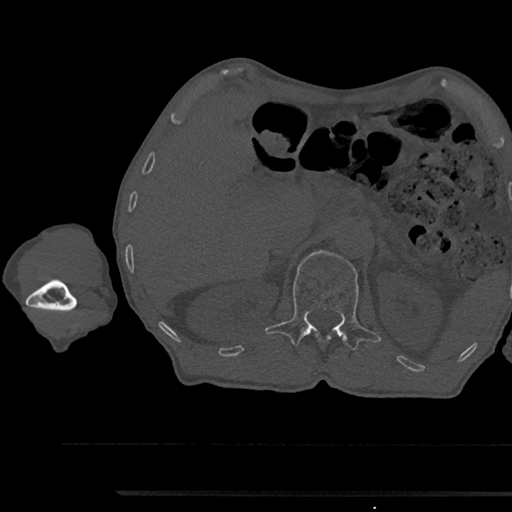
CT including the spine, one axial slice. Slice 653 of 797 in the series (ordered by position). Reconstruction kernel Br40s/3. 120 kVp. Bone window (W 1800 / L 400 HU). 512 × 512 image matrix, field of view 367 × 367 mm. Male patient, age 79 years. Case-level facts recorded for this patient, not image findings: primary cancer: prostate.
Annotated regions visible in this slice (semi-automatically segmented with operator editing):
- L1 vertebra: box from (x=265, y=250) to (x=381, y=350) px